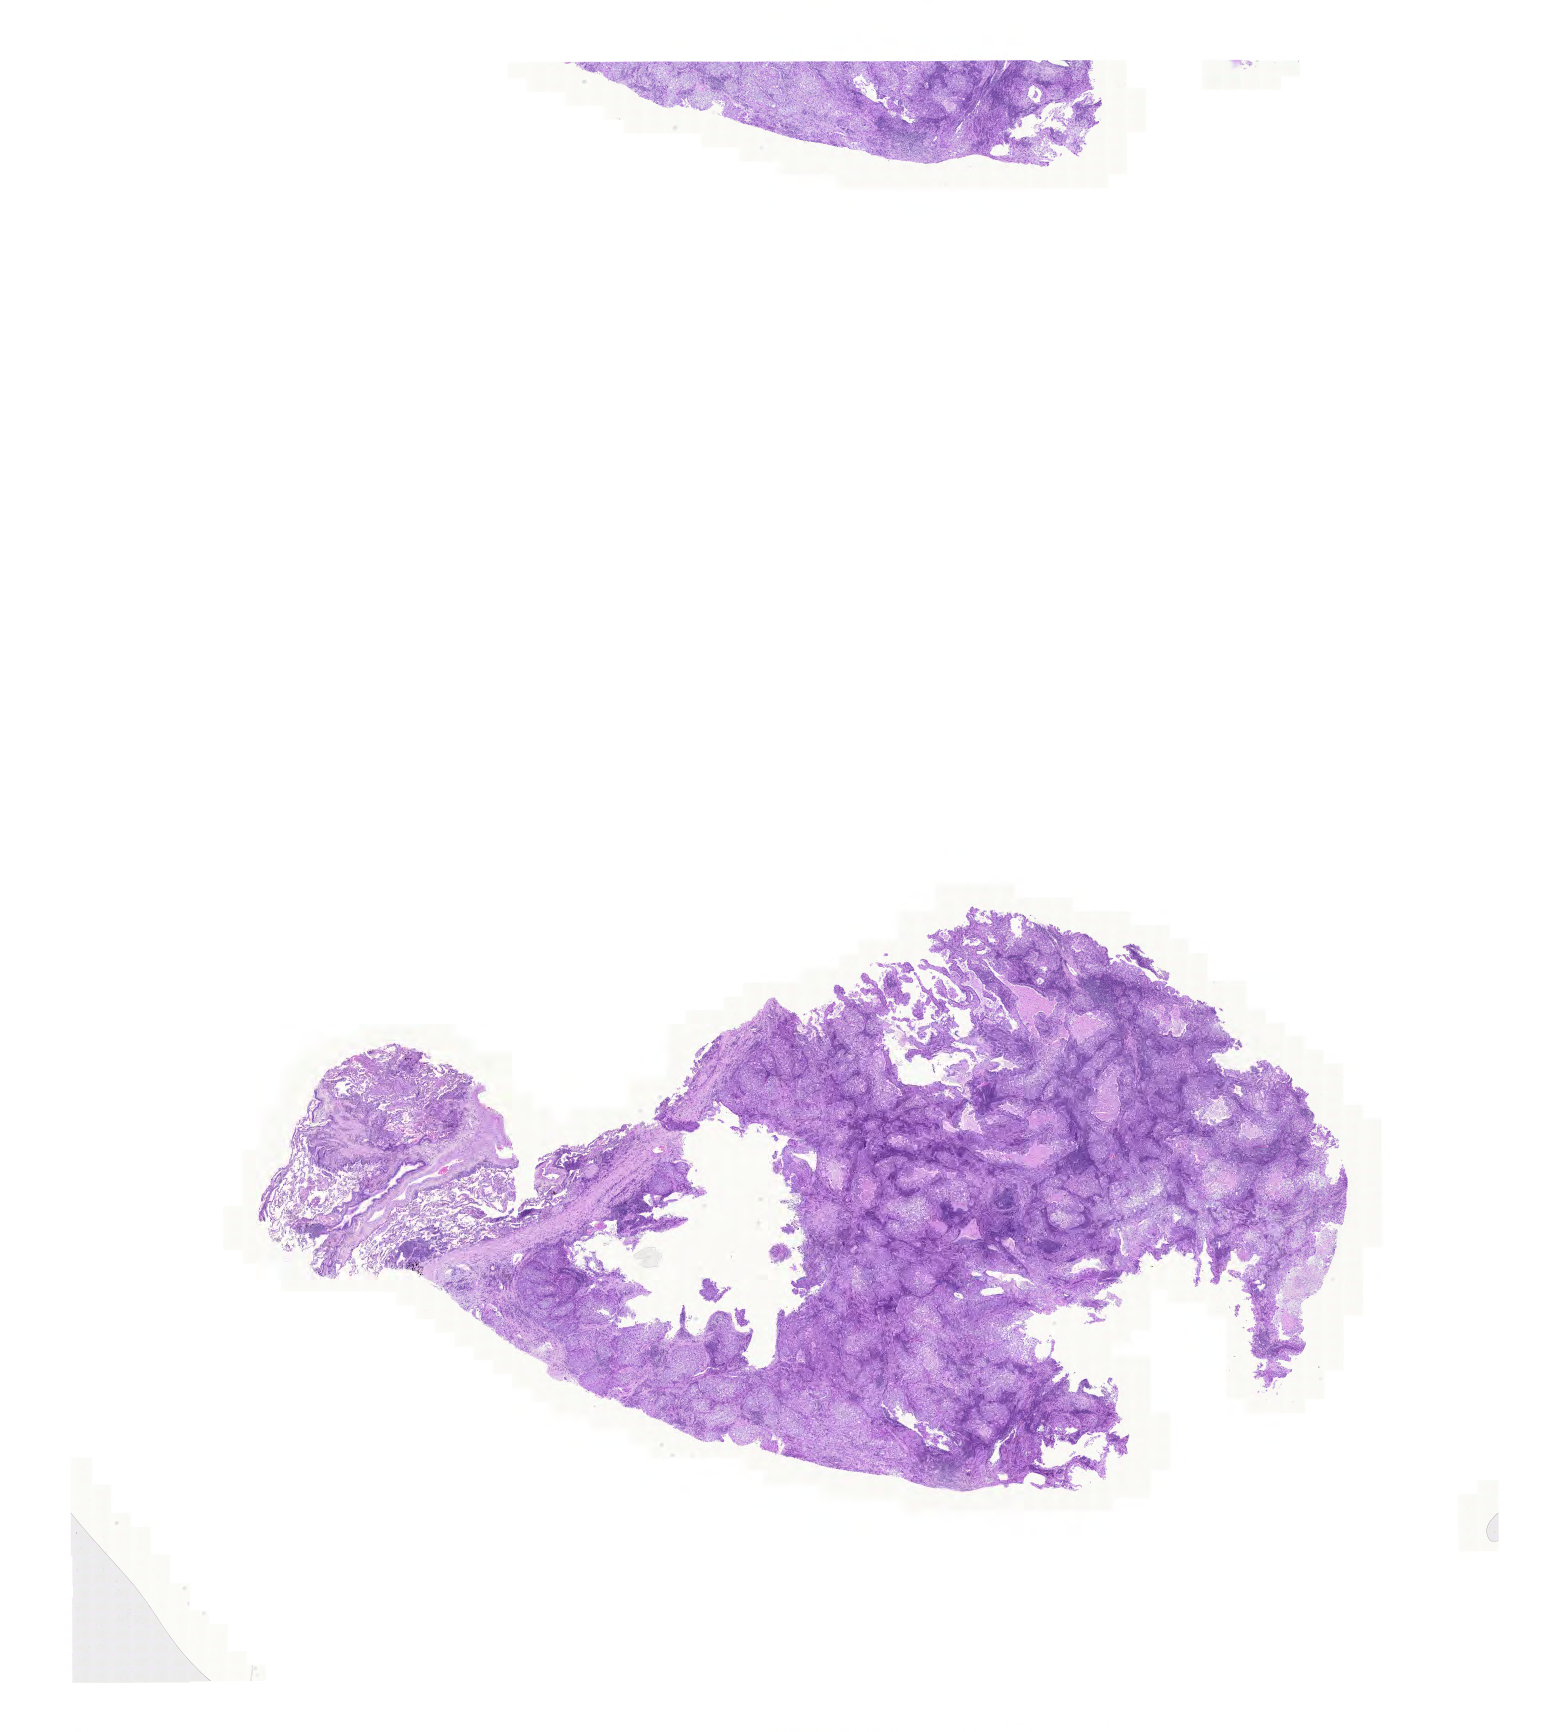
Digitized H&E tissue section (whole slide) — whole scanned area (about 23.1 x 25.8 mm, slide scanned at 20x) shown as a low-resolution overview. Formalin-fixed paraffin-embedded (FFPE) diagnostic section. Lung, primary tumour sample. Male, age 69 years at initial diagnosis.
- AJCC pathologic stage: IIIA
- diagnosis: Adenocarcinoma with mixed subtypes (lower lobe, lung)
- laterality: left